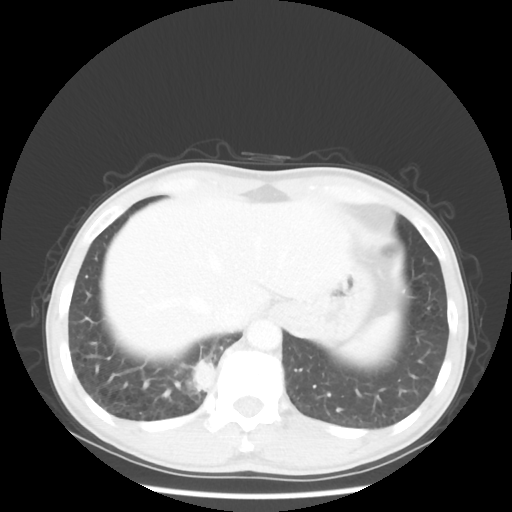
Chest CT, one axial slice. Slice 7 of 58 in the series (ordered by position). Reconstruction kernel STANDARD. Lung window (W 1500 / L -600 HU). 5 mm slice thickness. 512 × 512 image matrix. Male patient, age 56 years. Case-level facts recorded for this patient, not image findings: clinical TNM (as recorded): T2 N1 M1; histopathological grade: G1.
Outlined on this slice (rectangle marked by the reading radiologist):
- lung tumour (recorded histology: adenocarcinoma): box from (x=189, y=356) to (x=216, y=395) px